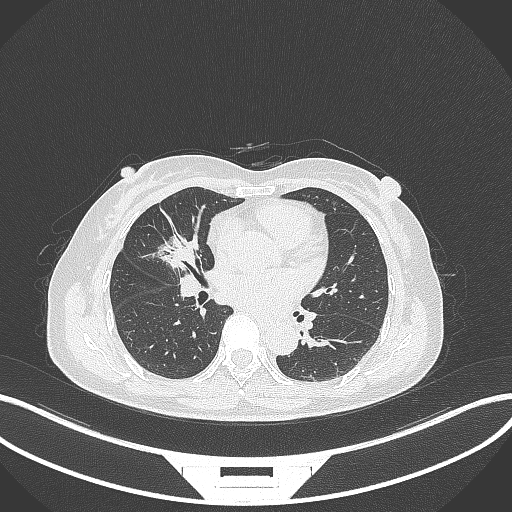
Chest CT, one axial slice; slice 148 of 284 in the series (ordered by position); 120 kVp; lung window (W 1500 / L -600 HU); 1 mm slice thickness; 512 × 512 image matrix. Patient: female, 51 years. From the clinical record (not read from this slice): clinical TNM (as recorded): T1c N0 M0; histopathological grade: G2.
Annotated regions visible in this slice (bounding box drawn by a radiologist):
- lung tumour (recorded histology: adenocarcinoma): bounding box (x1, y1, x2, y2) in pixels: (158, 230, 197, 271)